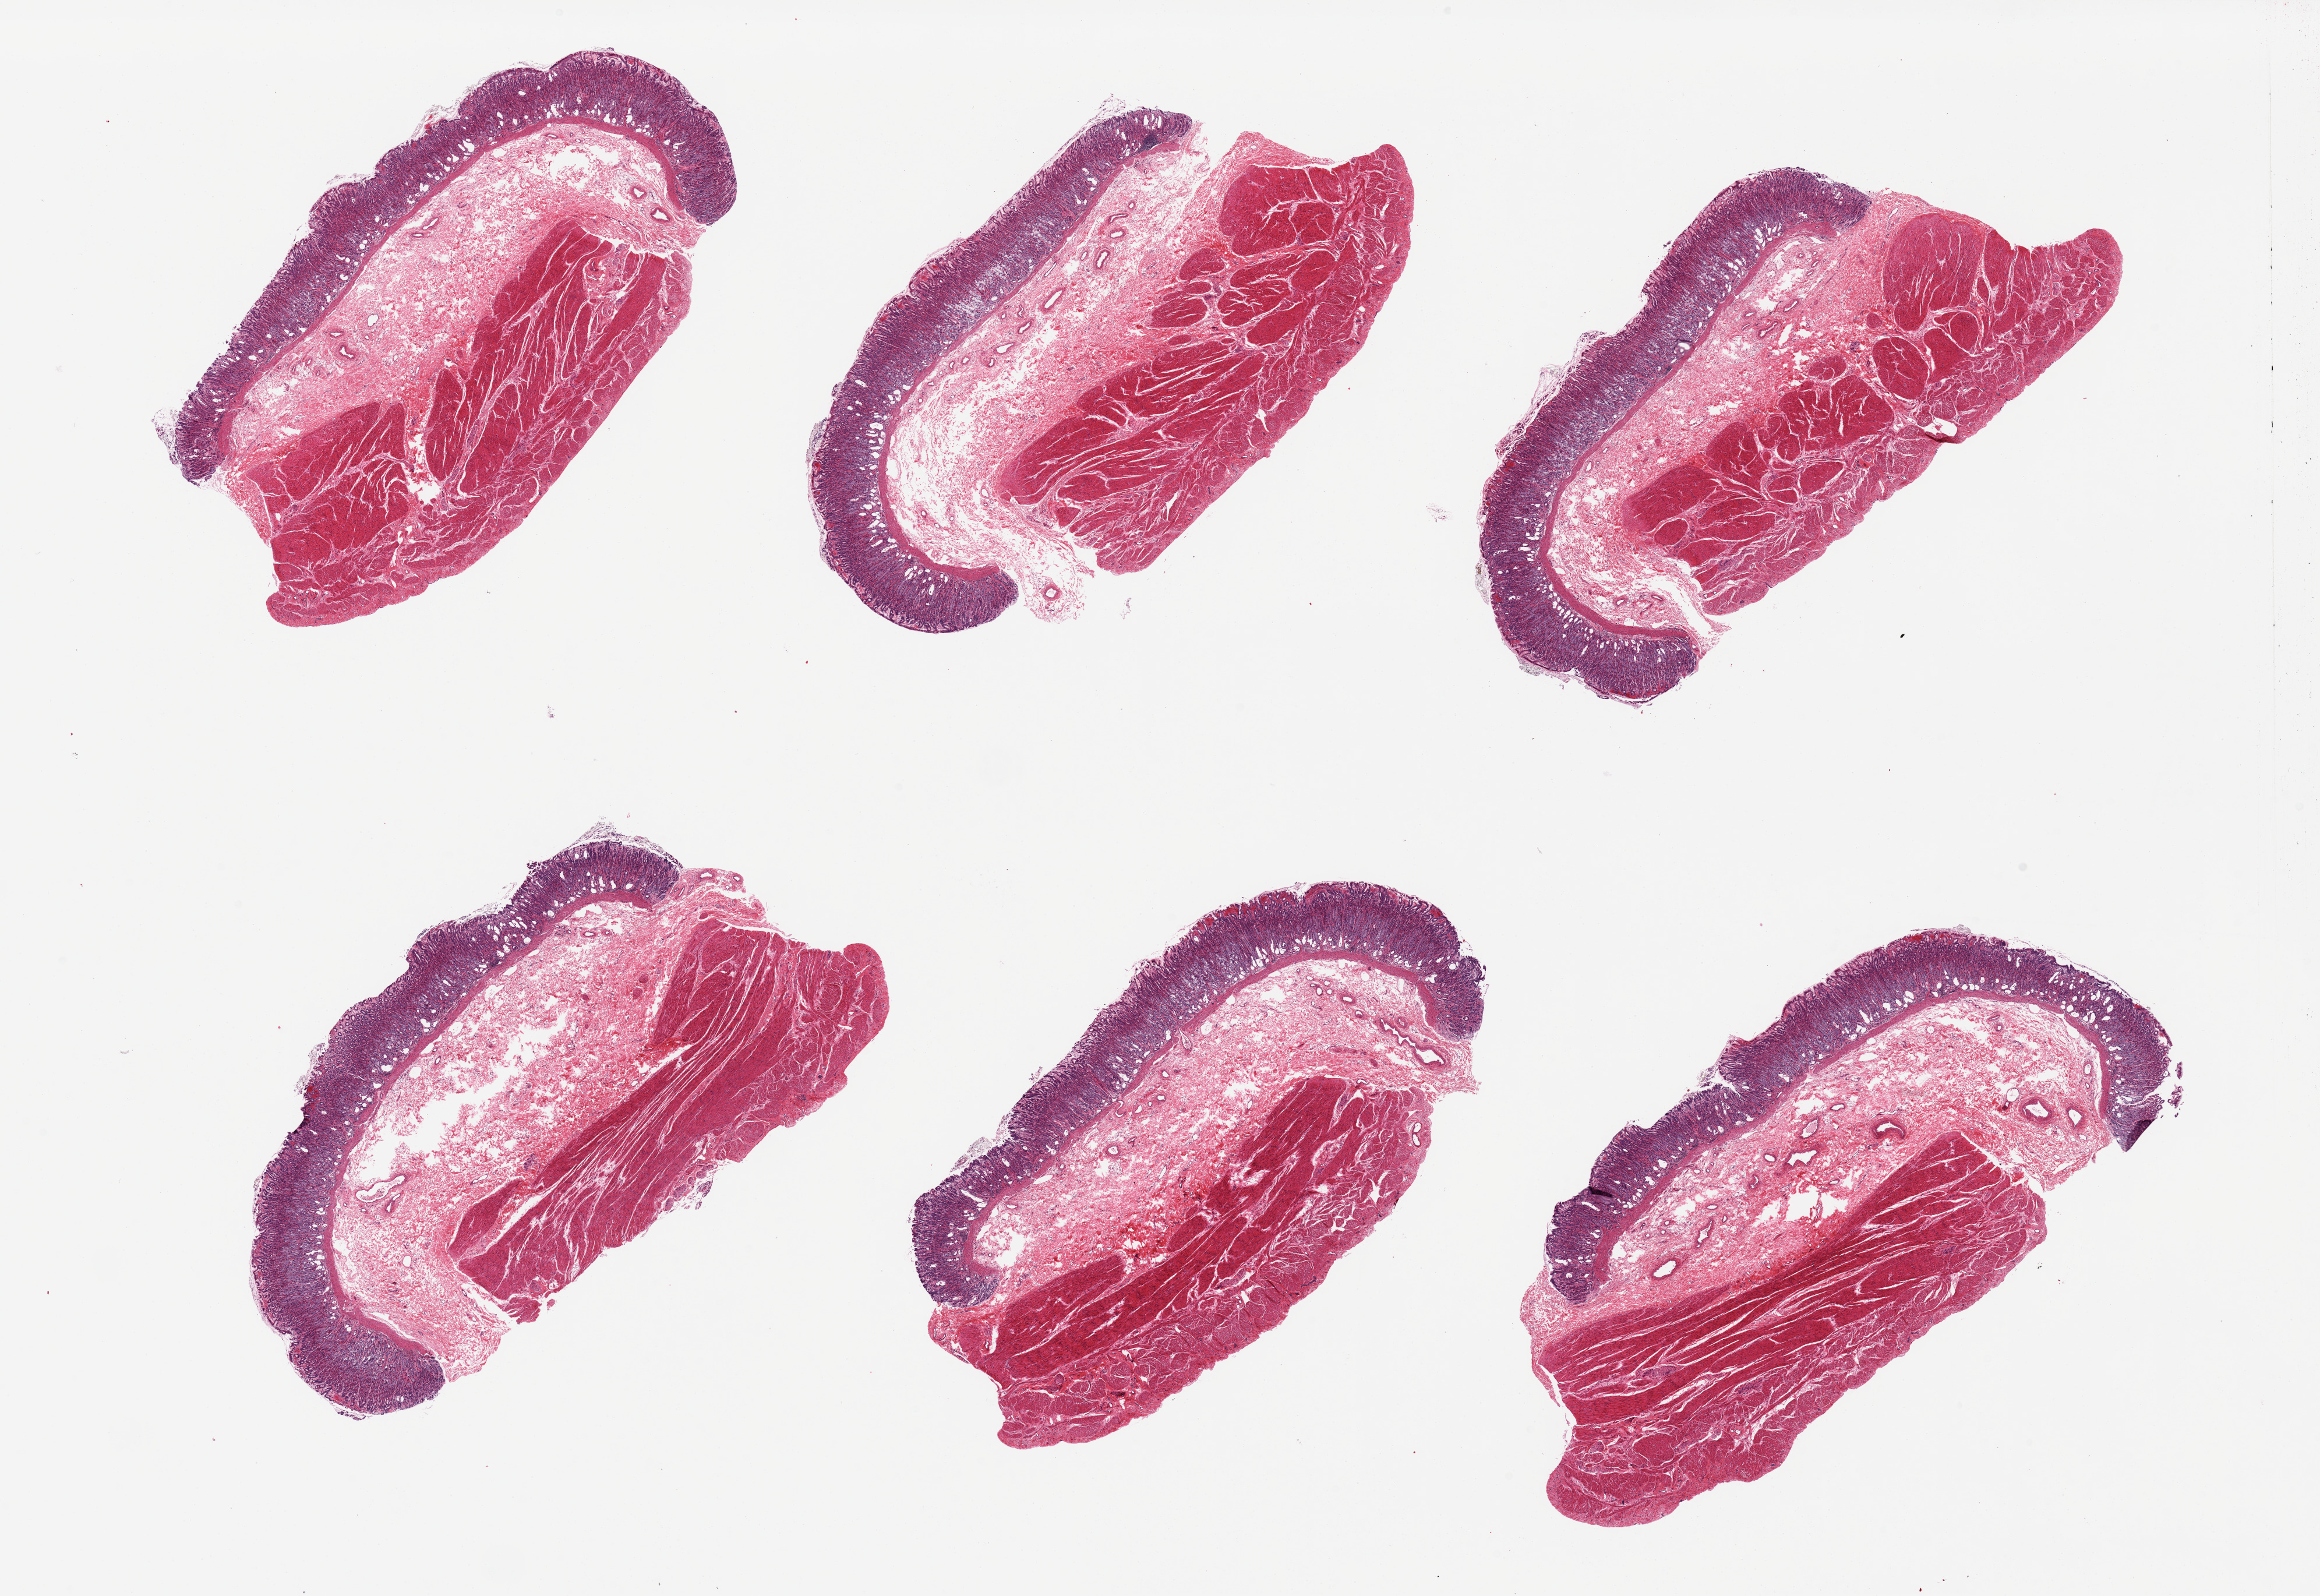
Haematoxylin and eosin whole-slide image, brightfield, shown as a low-resolution overview of the whole scanned area (about 31.5 x 21.7 mm). PAXgene-fixed paraffin-embedded (PFPE) section. Sampled site (target tissue): stomach. Tissue donor sample. Donor: male.
* reviewer comment on this tissue sample: 6 pieces; dilated deep glands (chief cell degeneration)